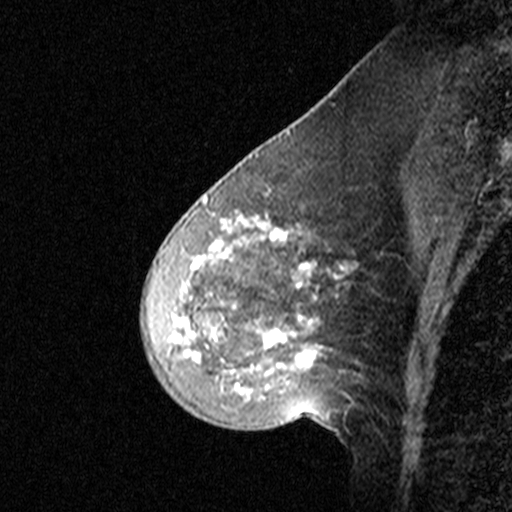
Breast MRI (dynamic contrast-enhanced), one sagittal slice; slice 16 of 44 in the series (ordered by position); dynamic contrast-enhanced study with each time point stored as its own series, time point 2 of 3 at this slice position (early post-contrast, ordered by acquisition time); 1.5 T; TE 4.5 ms, TR 11 ms; 512 × 512 image matrix, field of view 200 × 200 mm. Female patient, age 46 years. Case-level facts recorded for this patient, not image findings: setting: breast cancer imaged before/during neoadjuvant chemotherapy; receptor status: HER2-positive.
Outlined on this slice (semi-automatically segmented with operator editing):
- analysis volume of interest (the breast-tissue region the enhancement analysis was run in; not a lesion): bounding box [x1, y1, x2, y2] px = [144, 172, 359, 393]
- tumour enhancement mask (voxels above the 90 % enhancement threshold inside the analysis volume of interest): [179, 198, 347, 378]